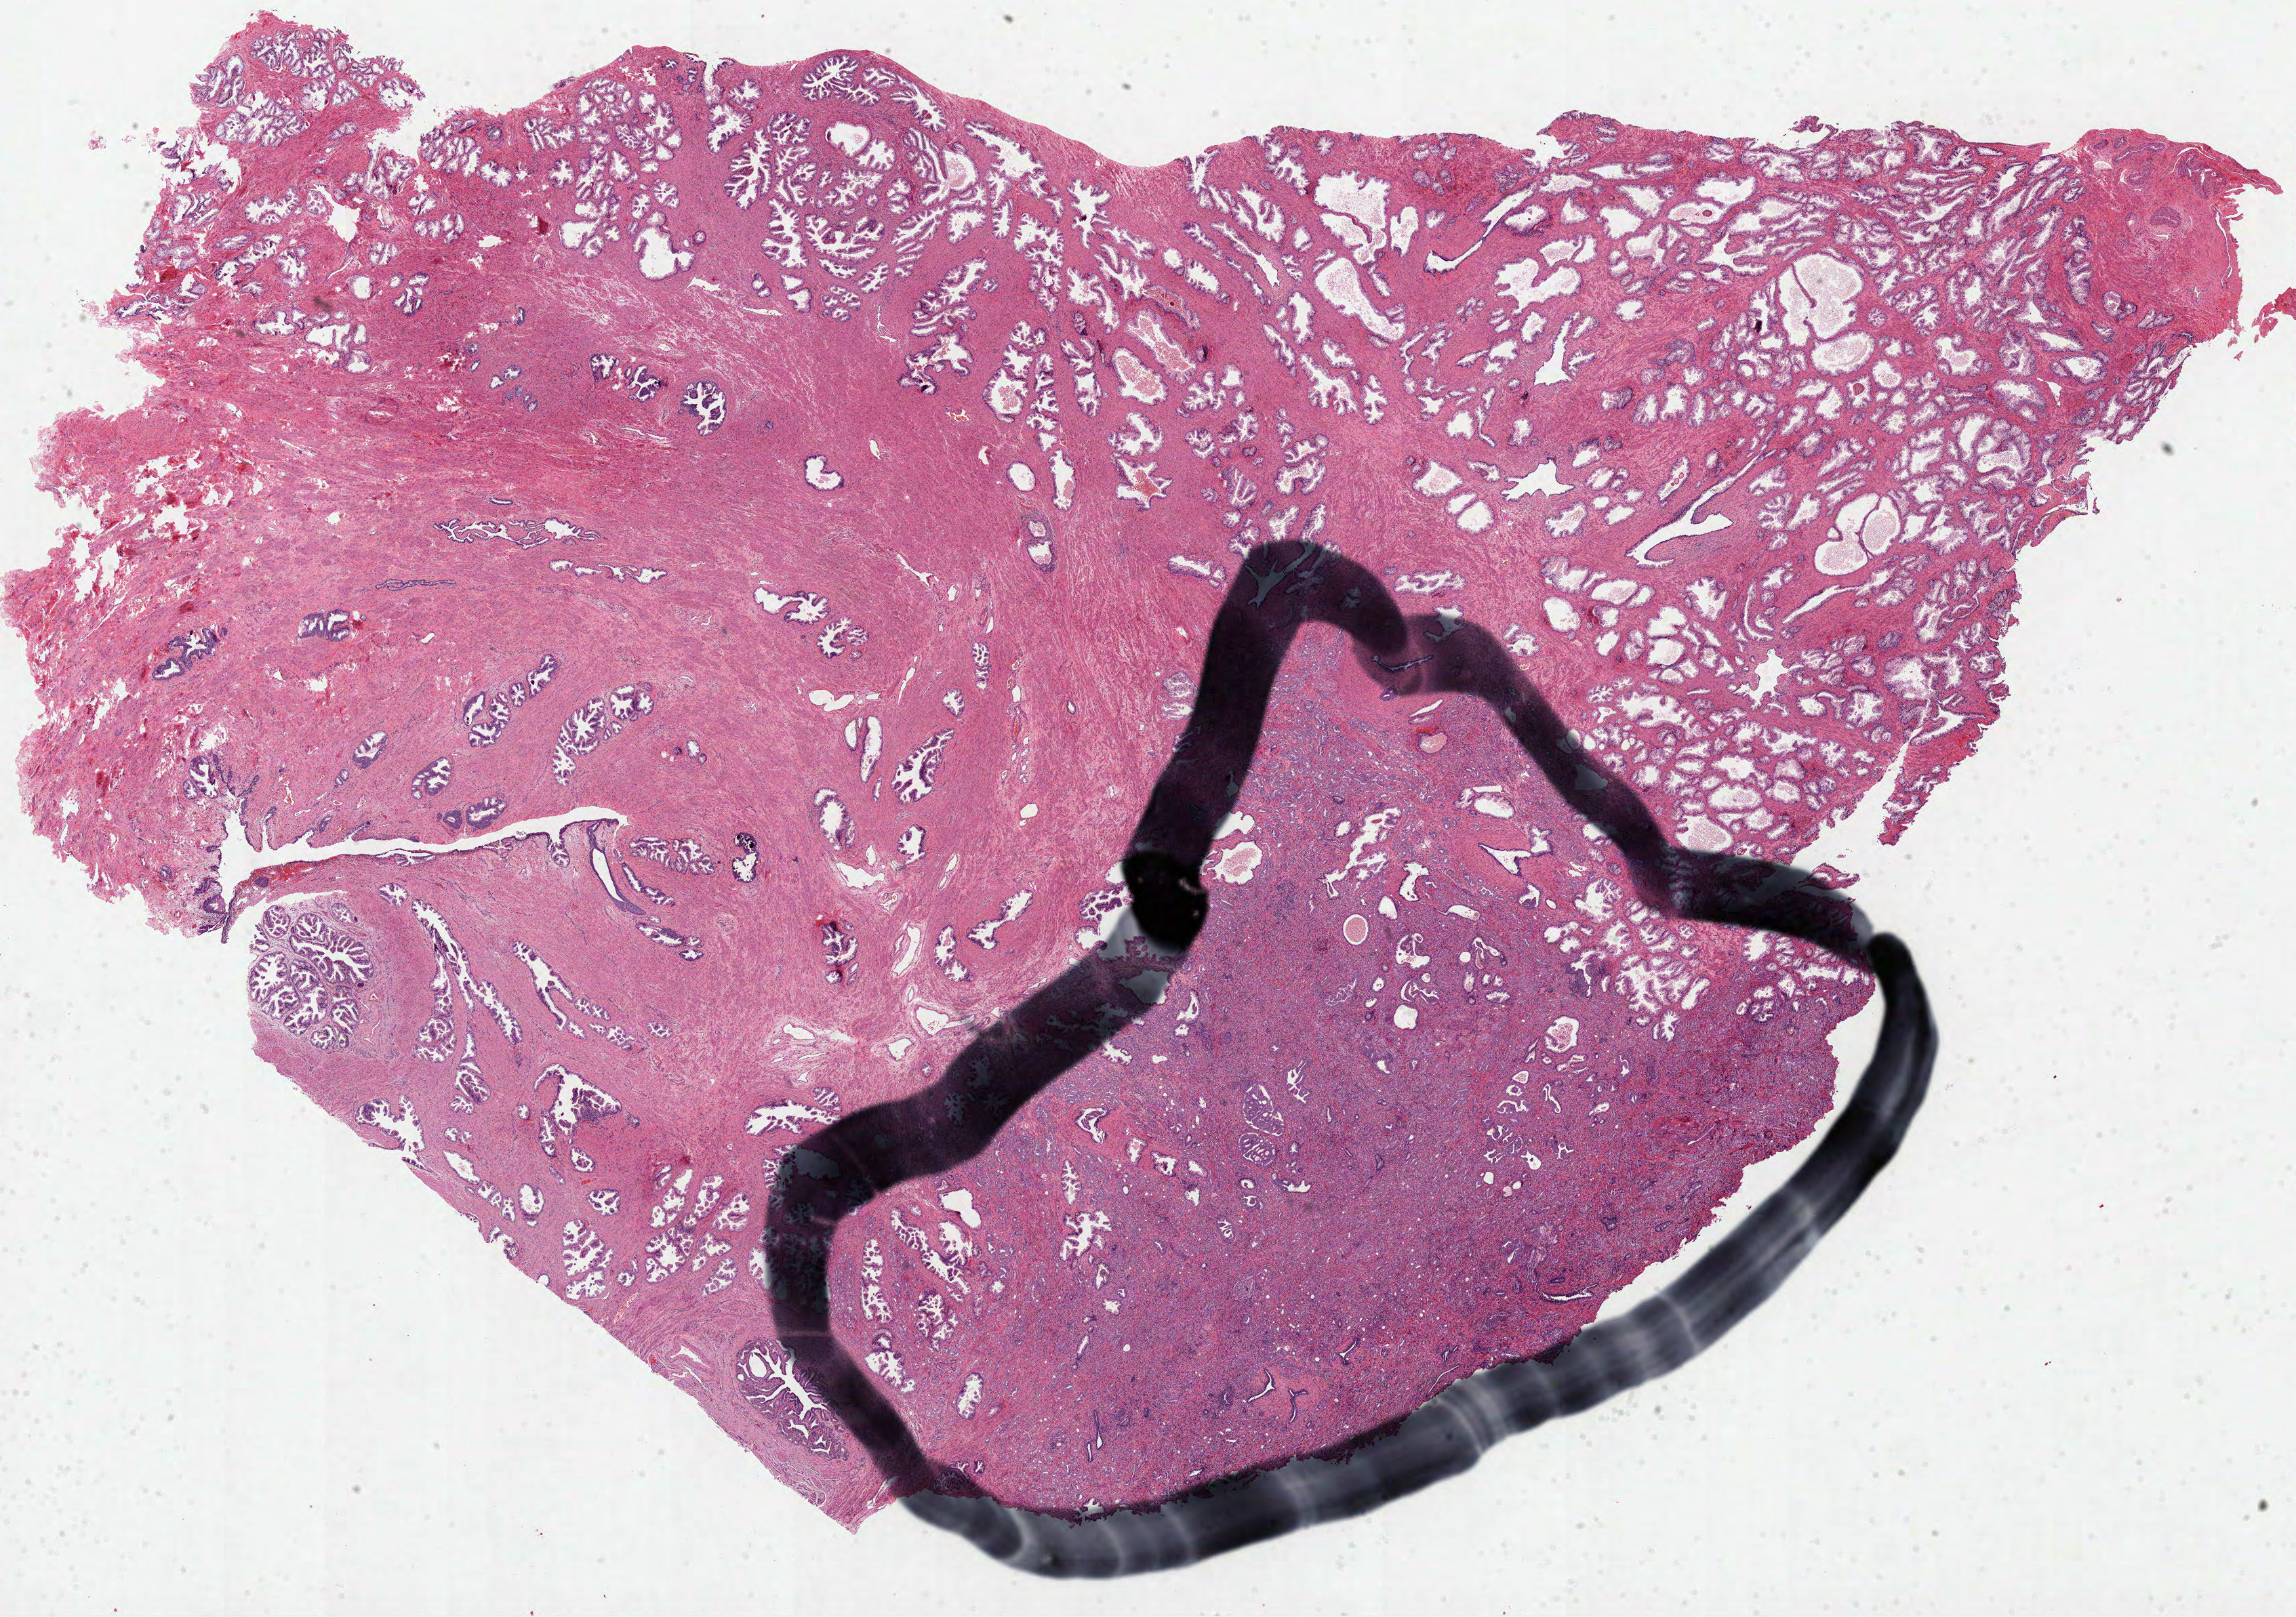
H&E whole-slide image, a low-resolution overview of the entire scanned area, about 27.3 x 19.2 mm (slide scanned at 40x), formalin-fixed paraffin-embedded (FFPE) diagnostic section, sample: primary tumour, prostate. Male patient; age at initial diagnosis 48 years. Gleason score: 7 (4+3).
• pathologic diagnosis: Acinar cell carcinoma (prostate gland)